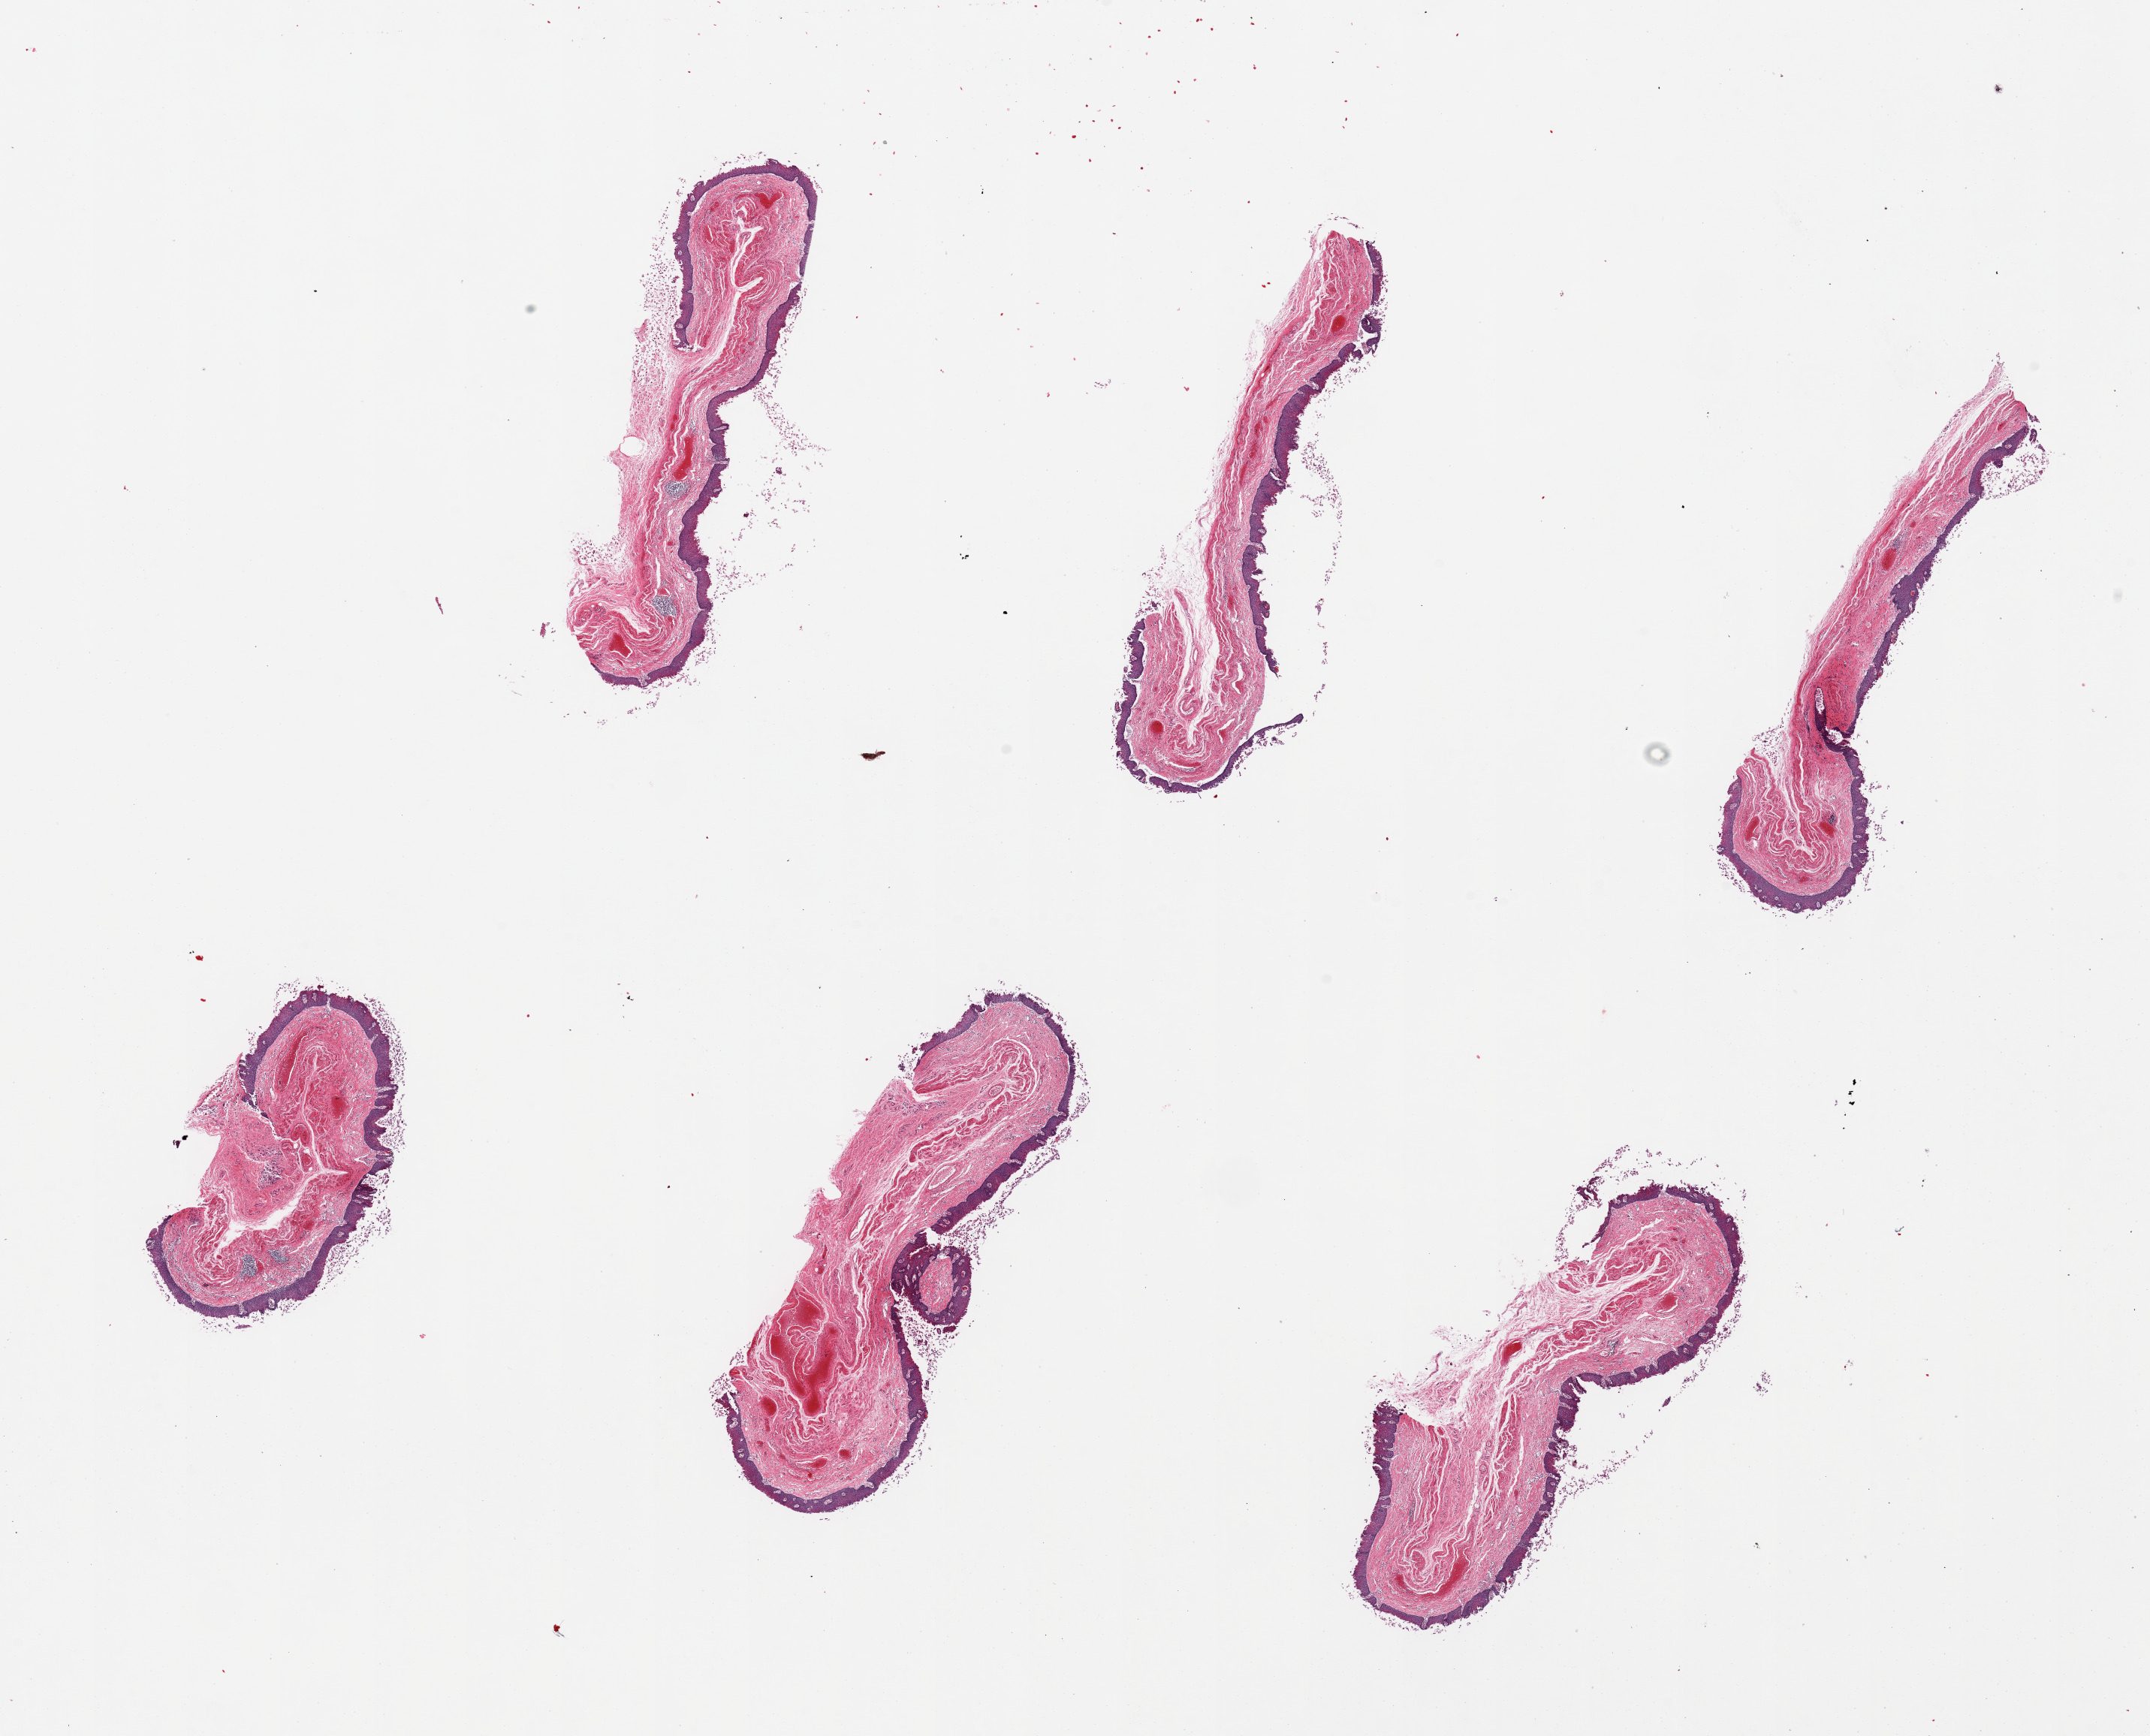
Whole-slide image, haematoxylin and eosin stain, brightfield — whole scanned area (about 22.6 x 18.3 mm) shown as a low-resolution overview. PAXgene-fixed paraffin-embedded (PFPE) section. Section of esophageal mucous membrane (target tissue). Tissue donor sample. Donor: male.
Pathologist's review note for this sample: 6 pieces, squamous mucosa partly sloughed.